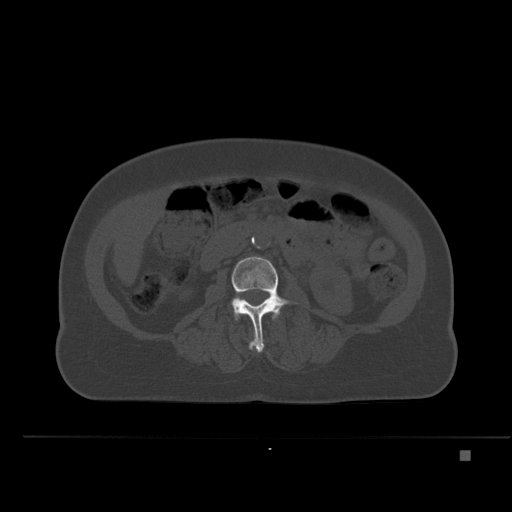
CT including the spine, one axial slice; slice 196 of 477 in the series (ordered by position); bone window (W 1800 / L 400 HU); 1.5 mm slice thickness; 512 × 512 image matrix, field of view 422 × 422 mm. Female patient, age 74 years. Case-level facts recorded for this patient, not image findings: primary cancer: colon.
Annotated regions visible in this slice (semi-automatic segmentation, software-assisted and operator-edited):
- L3 vertebra: bounding box (x1, y1, x2, y2) in pixels: (231, 257, 297, 352)